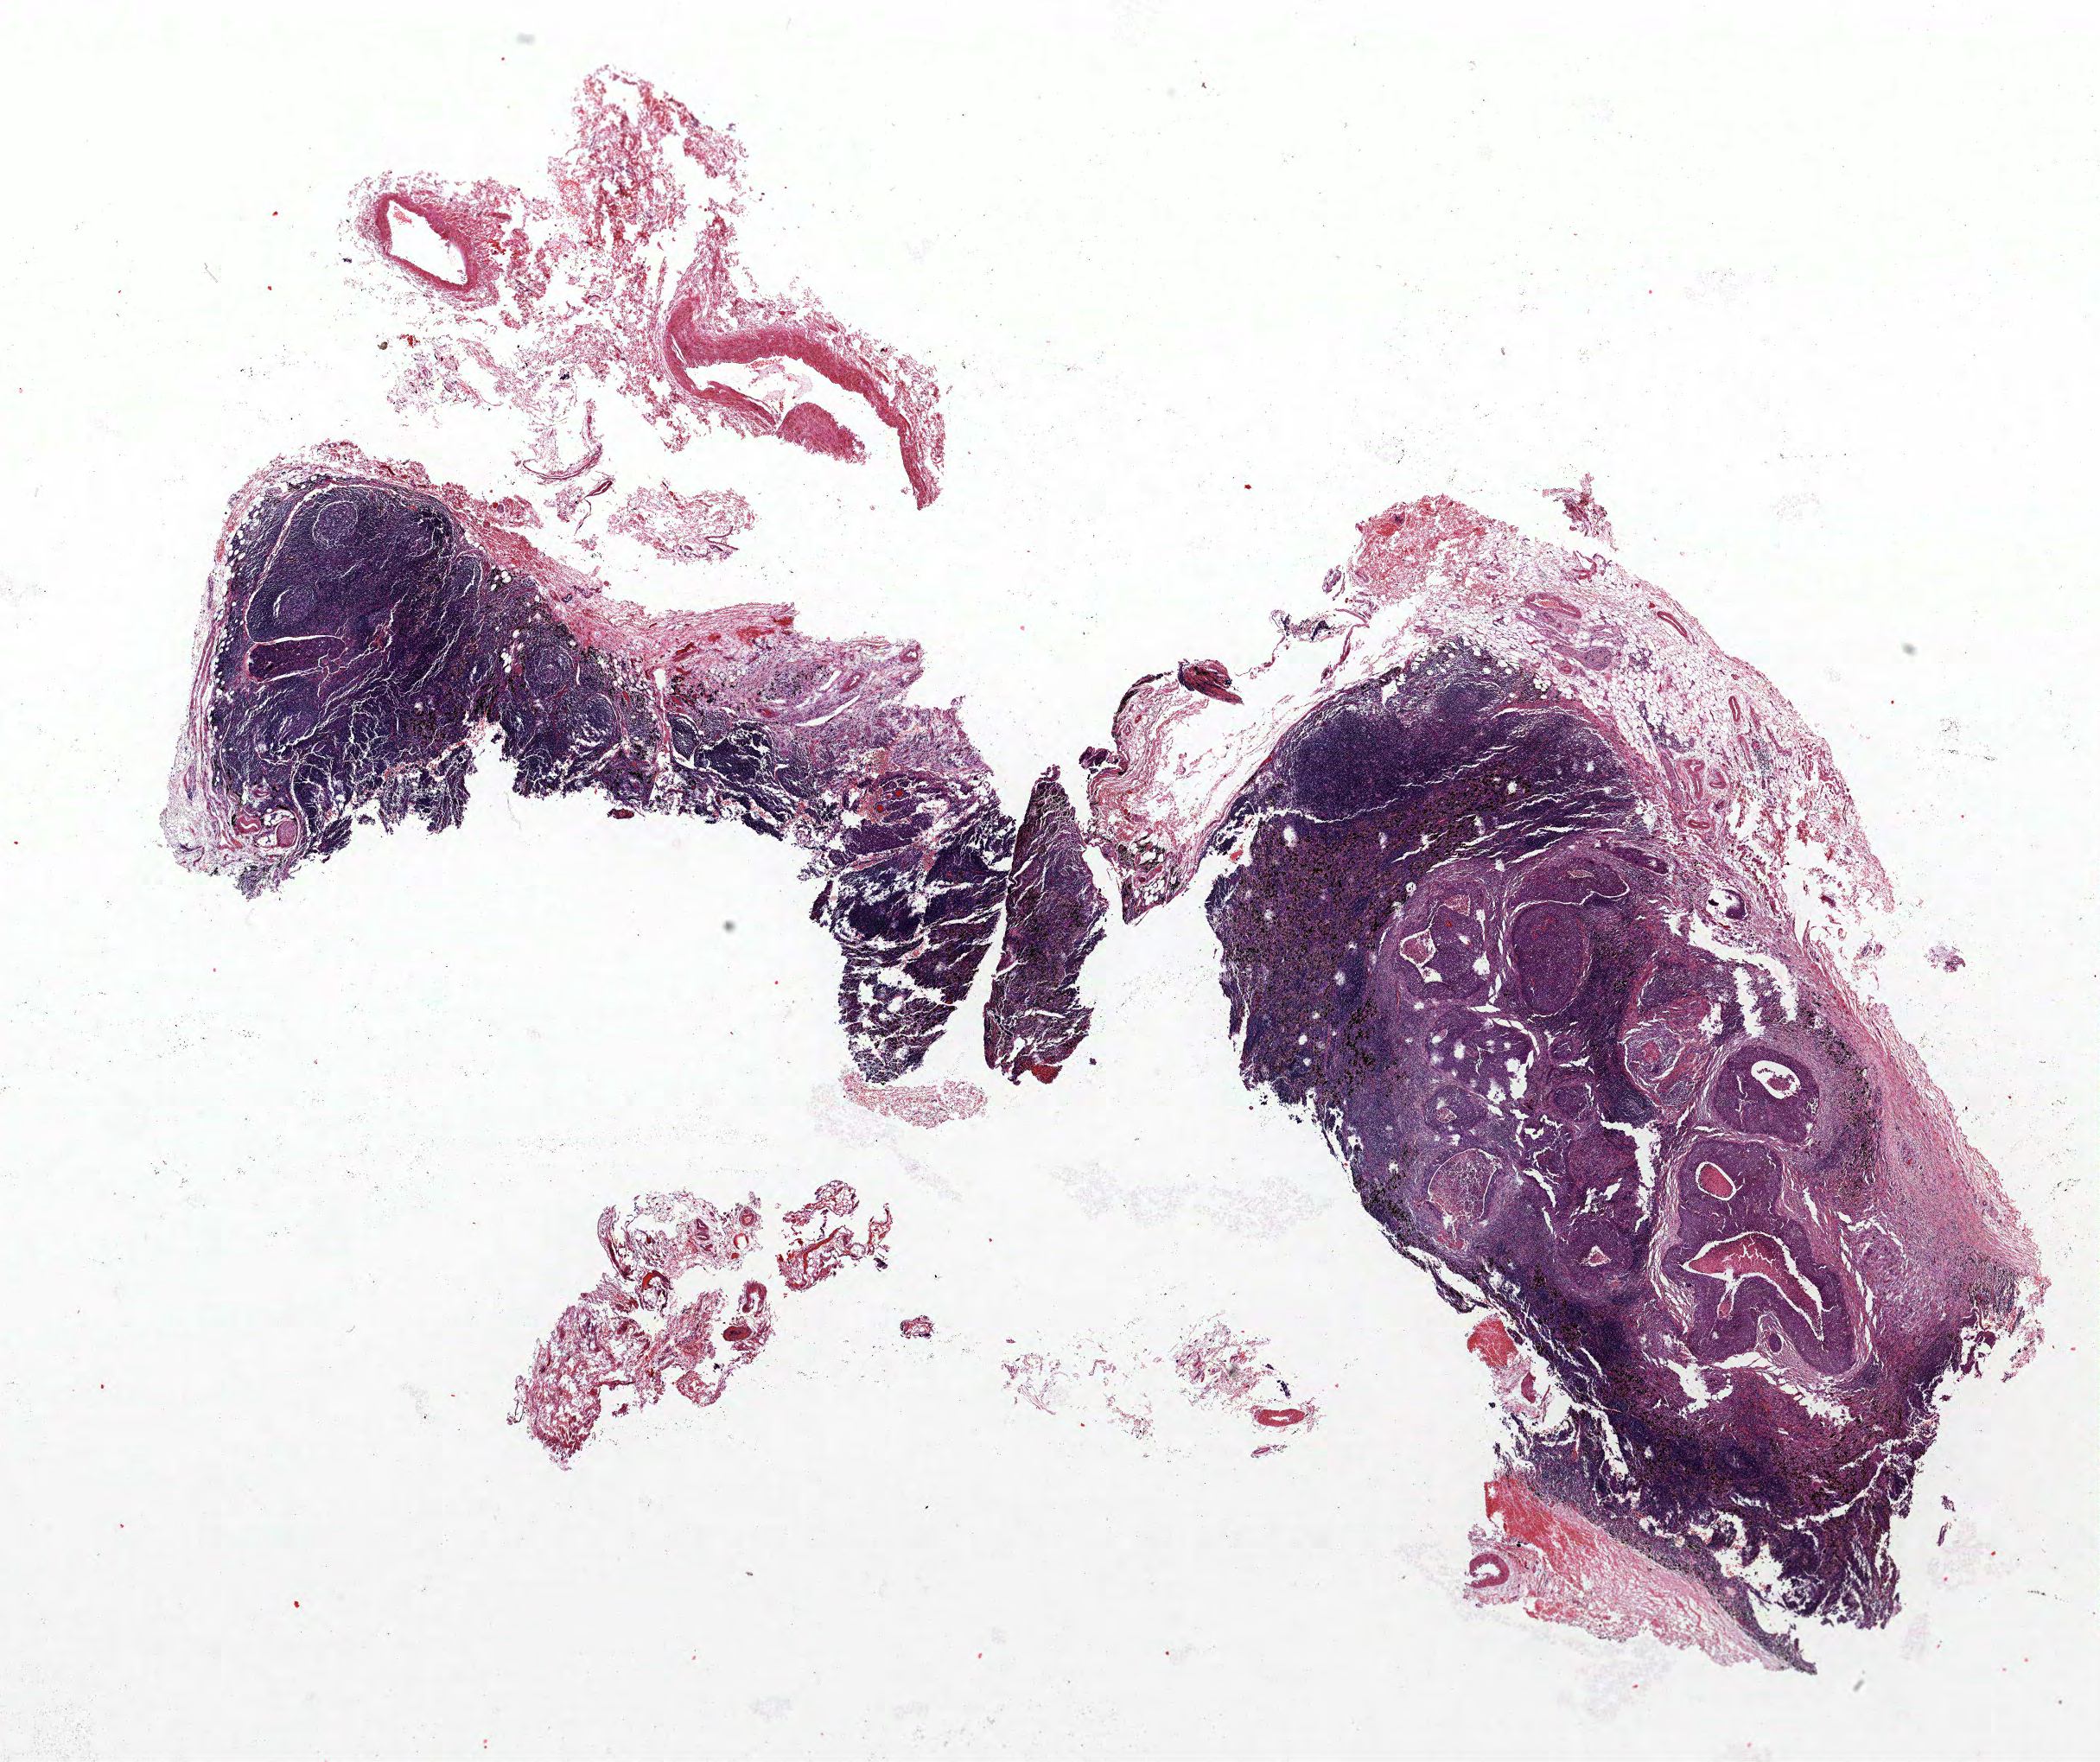
H&E whole-slide image — shown as a low-resolution overview of the whole scanned area (about 19.4 x 16.3 mm). Formalin-fixed paraffin-embedded (FFPE) section. Lung. Male, age 68 at enrolment. Current smoker at enrolment. Grade: moderately differentiated (G2).
- tumour size (pathology): 25 mm
- stage (AJCC 6th edition): IIA
- primary tumour location (clinical record): left upper lobe
- participant's lung-cancer diagnosis: Squamous cell carcinoma, NOS